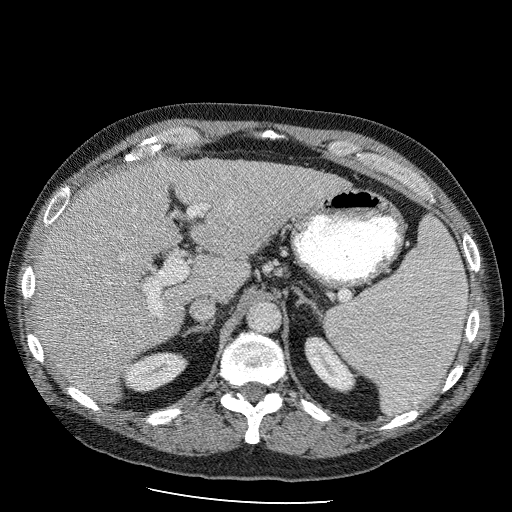
Contrast-enhanced abdominal CT (liver protocol), one axial slice. Slice 64 of 98 in the series (ordered by position). Reconstruction kernel STANDARD. 120 kVp. Soft-tissue window (W 400 / L 40 HU). 2.5 mm slice thickness. 512 × 512 image matrix. From the clinical record (not read from this slice): diagnosis: hepatocellular carcinoma (patient treated with transarterial chemoembolisation; whether this scan precedes or follows treatment is not stated here); TNM stage (as recorded): Stage-II; Child-Pugh class: B.
Outlined on this slice (semi-automatic segmentation, software-assisted and operator-edited):
- liver parenchyma outside the tumour (the mass and vessels are separate outlines, so this box may not span the whole liver): bounding box [x1, y1, x2, y2] px = [32, 156, 356, 406]
- liver vessels: [127, 188, 353, 331]